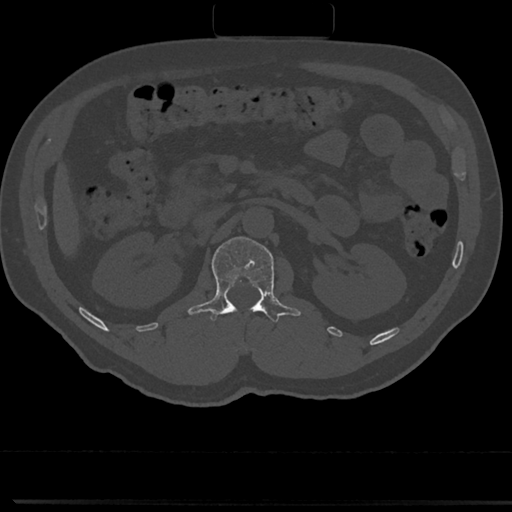
CT including the spine, one axial slice; slice 83 of 817 in the series (ordered by position); bone window (W 1800 / L 400 HU); 512 × 512 image matrix. Male patient, age 61 years. Case-level facts recorded for this patient, not image findings: primary cancer: prostate.
Outlined on this slice (semi-automatic segmentation, software-assisted and operator-edited):
- L1 vertebra: bounding box (x1, y1, x2, y2) in pixels: (191, 238, 298, 324)